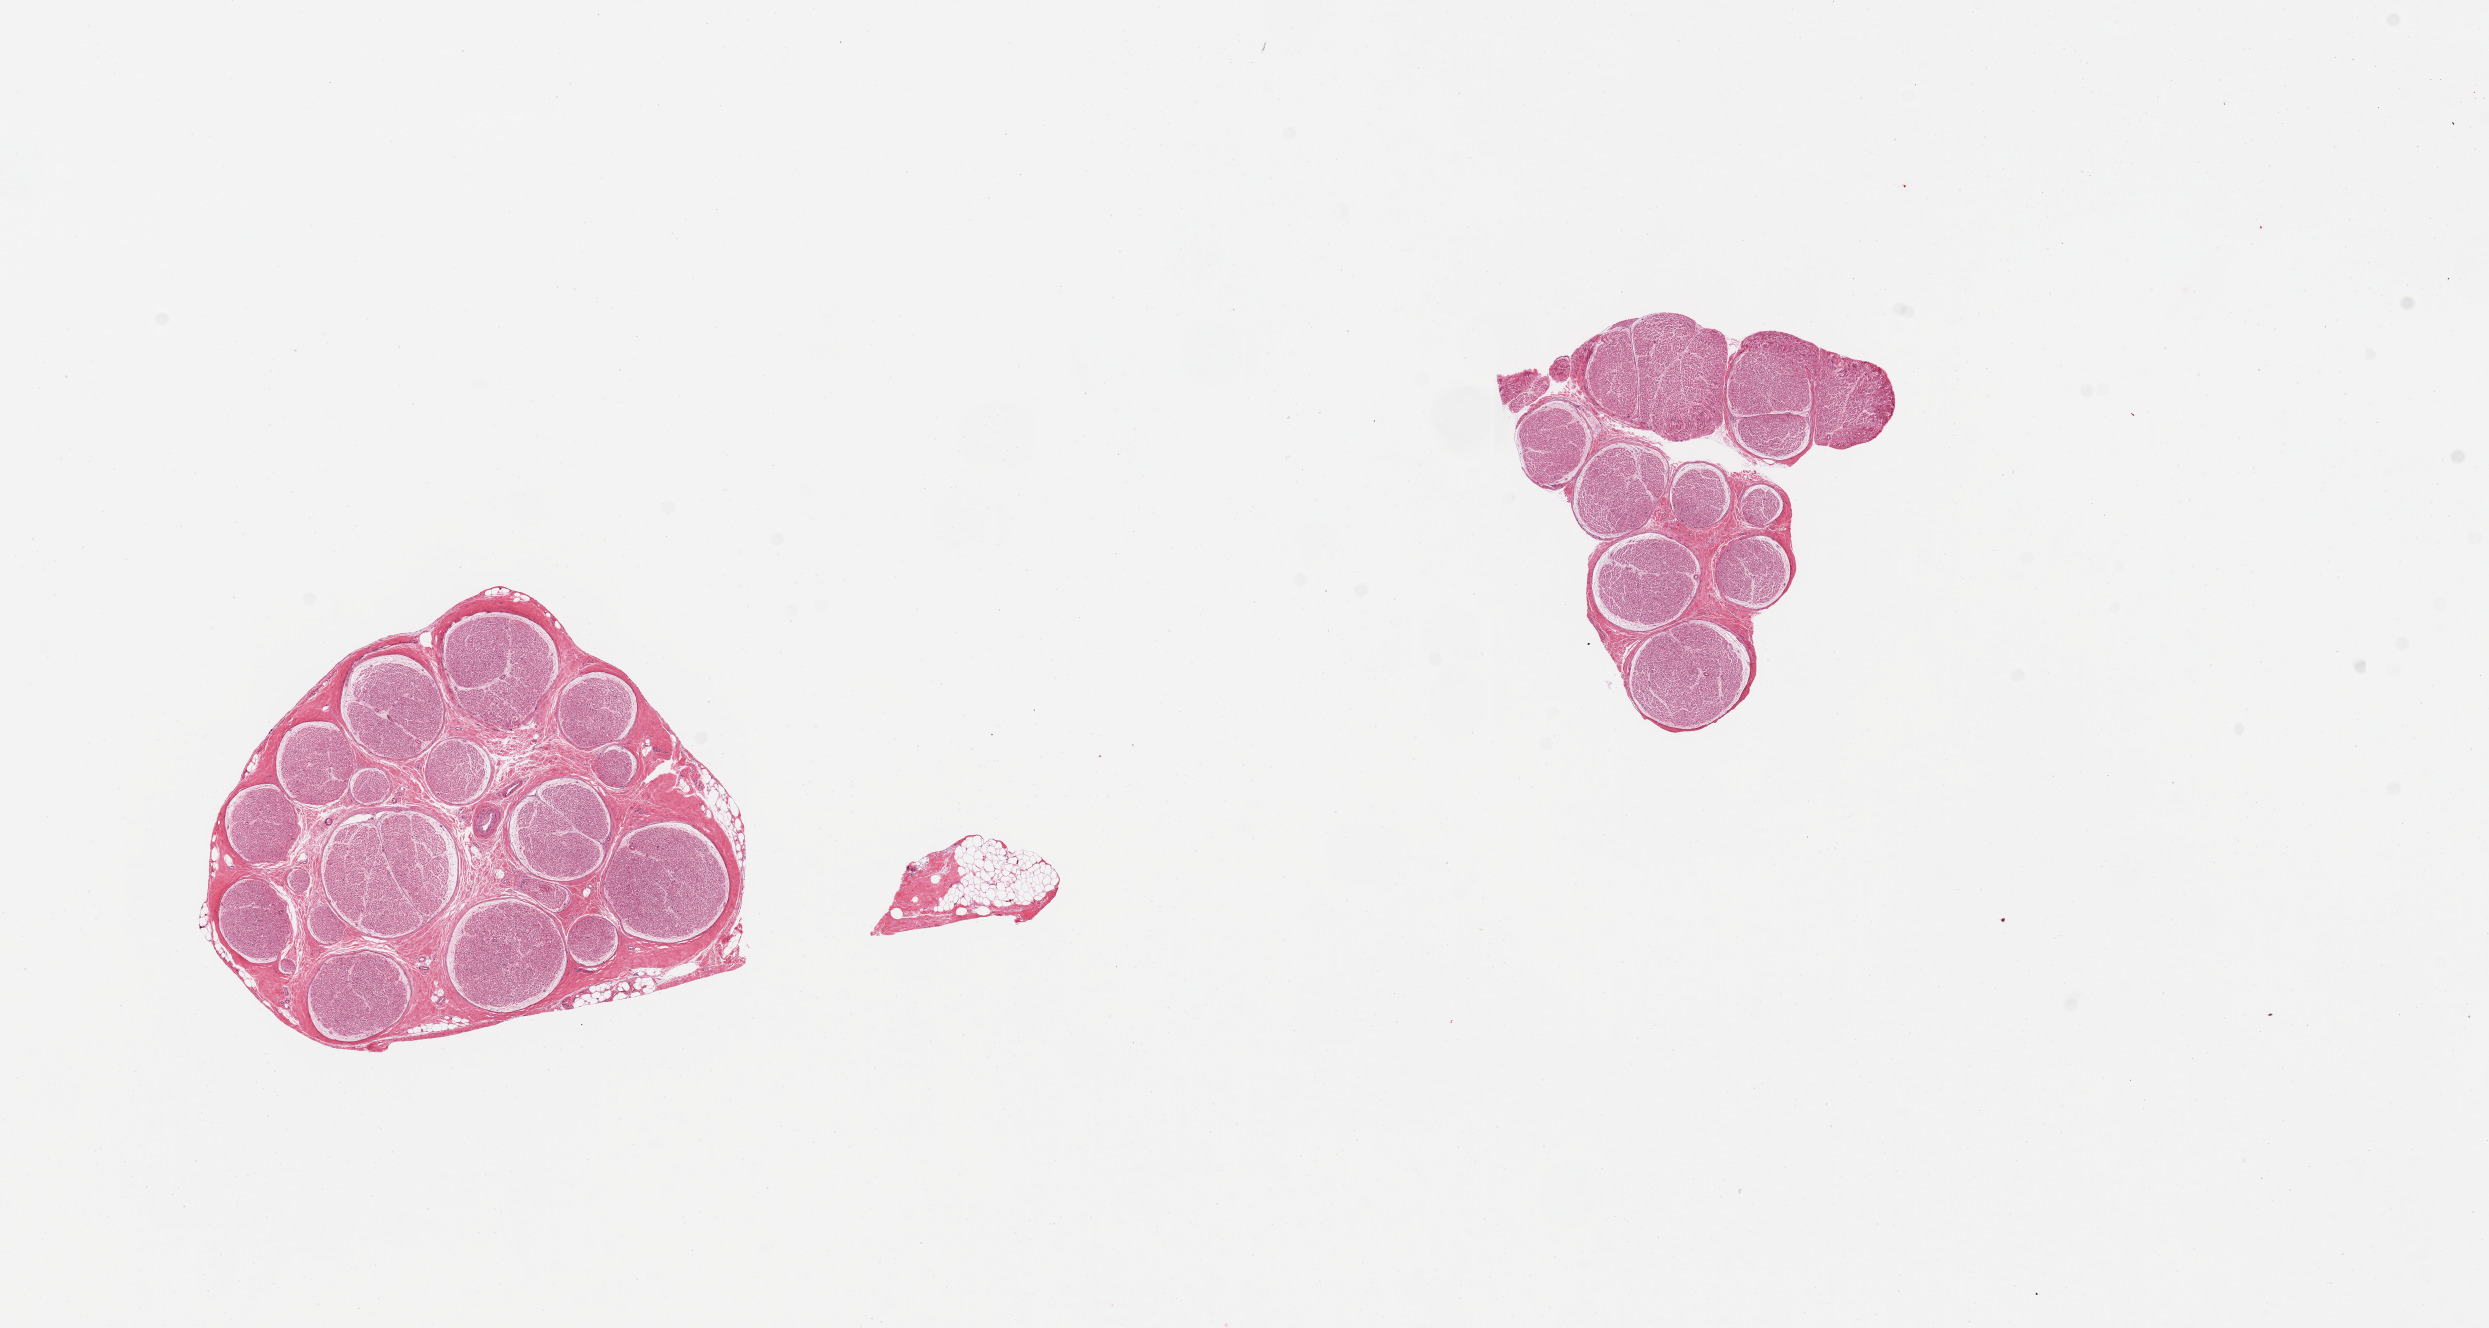
Digitized hematoxylin and eosin (H&E)-stained section, brightfield, a low-resolution overview of the entire scanned area, about 19.7 x 10.5 mm (slide scanned at 20x). PAXgene-fixed, paraffin-embedded tissue. Section of tibial nerve (target tissue). Tissue donor sample. Donor sex: male.
Pathologist's review note for this sample: 2 pieces, good clean specimens, minimal adherent fat.